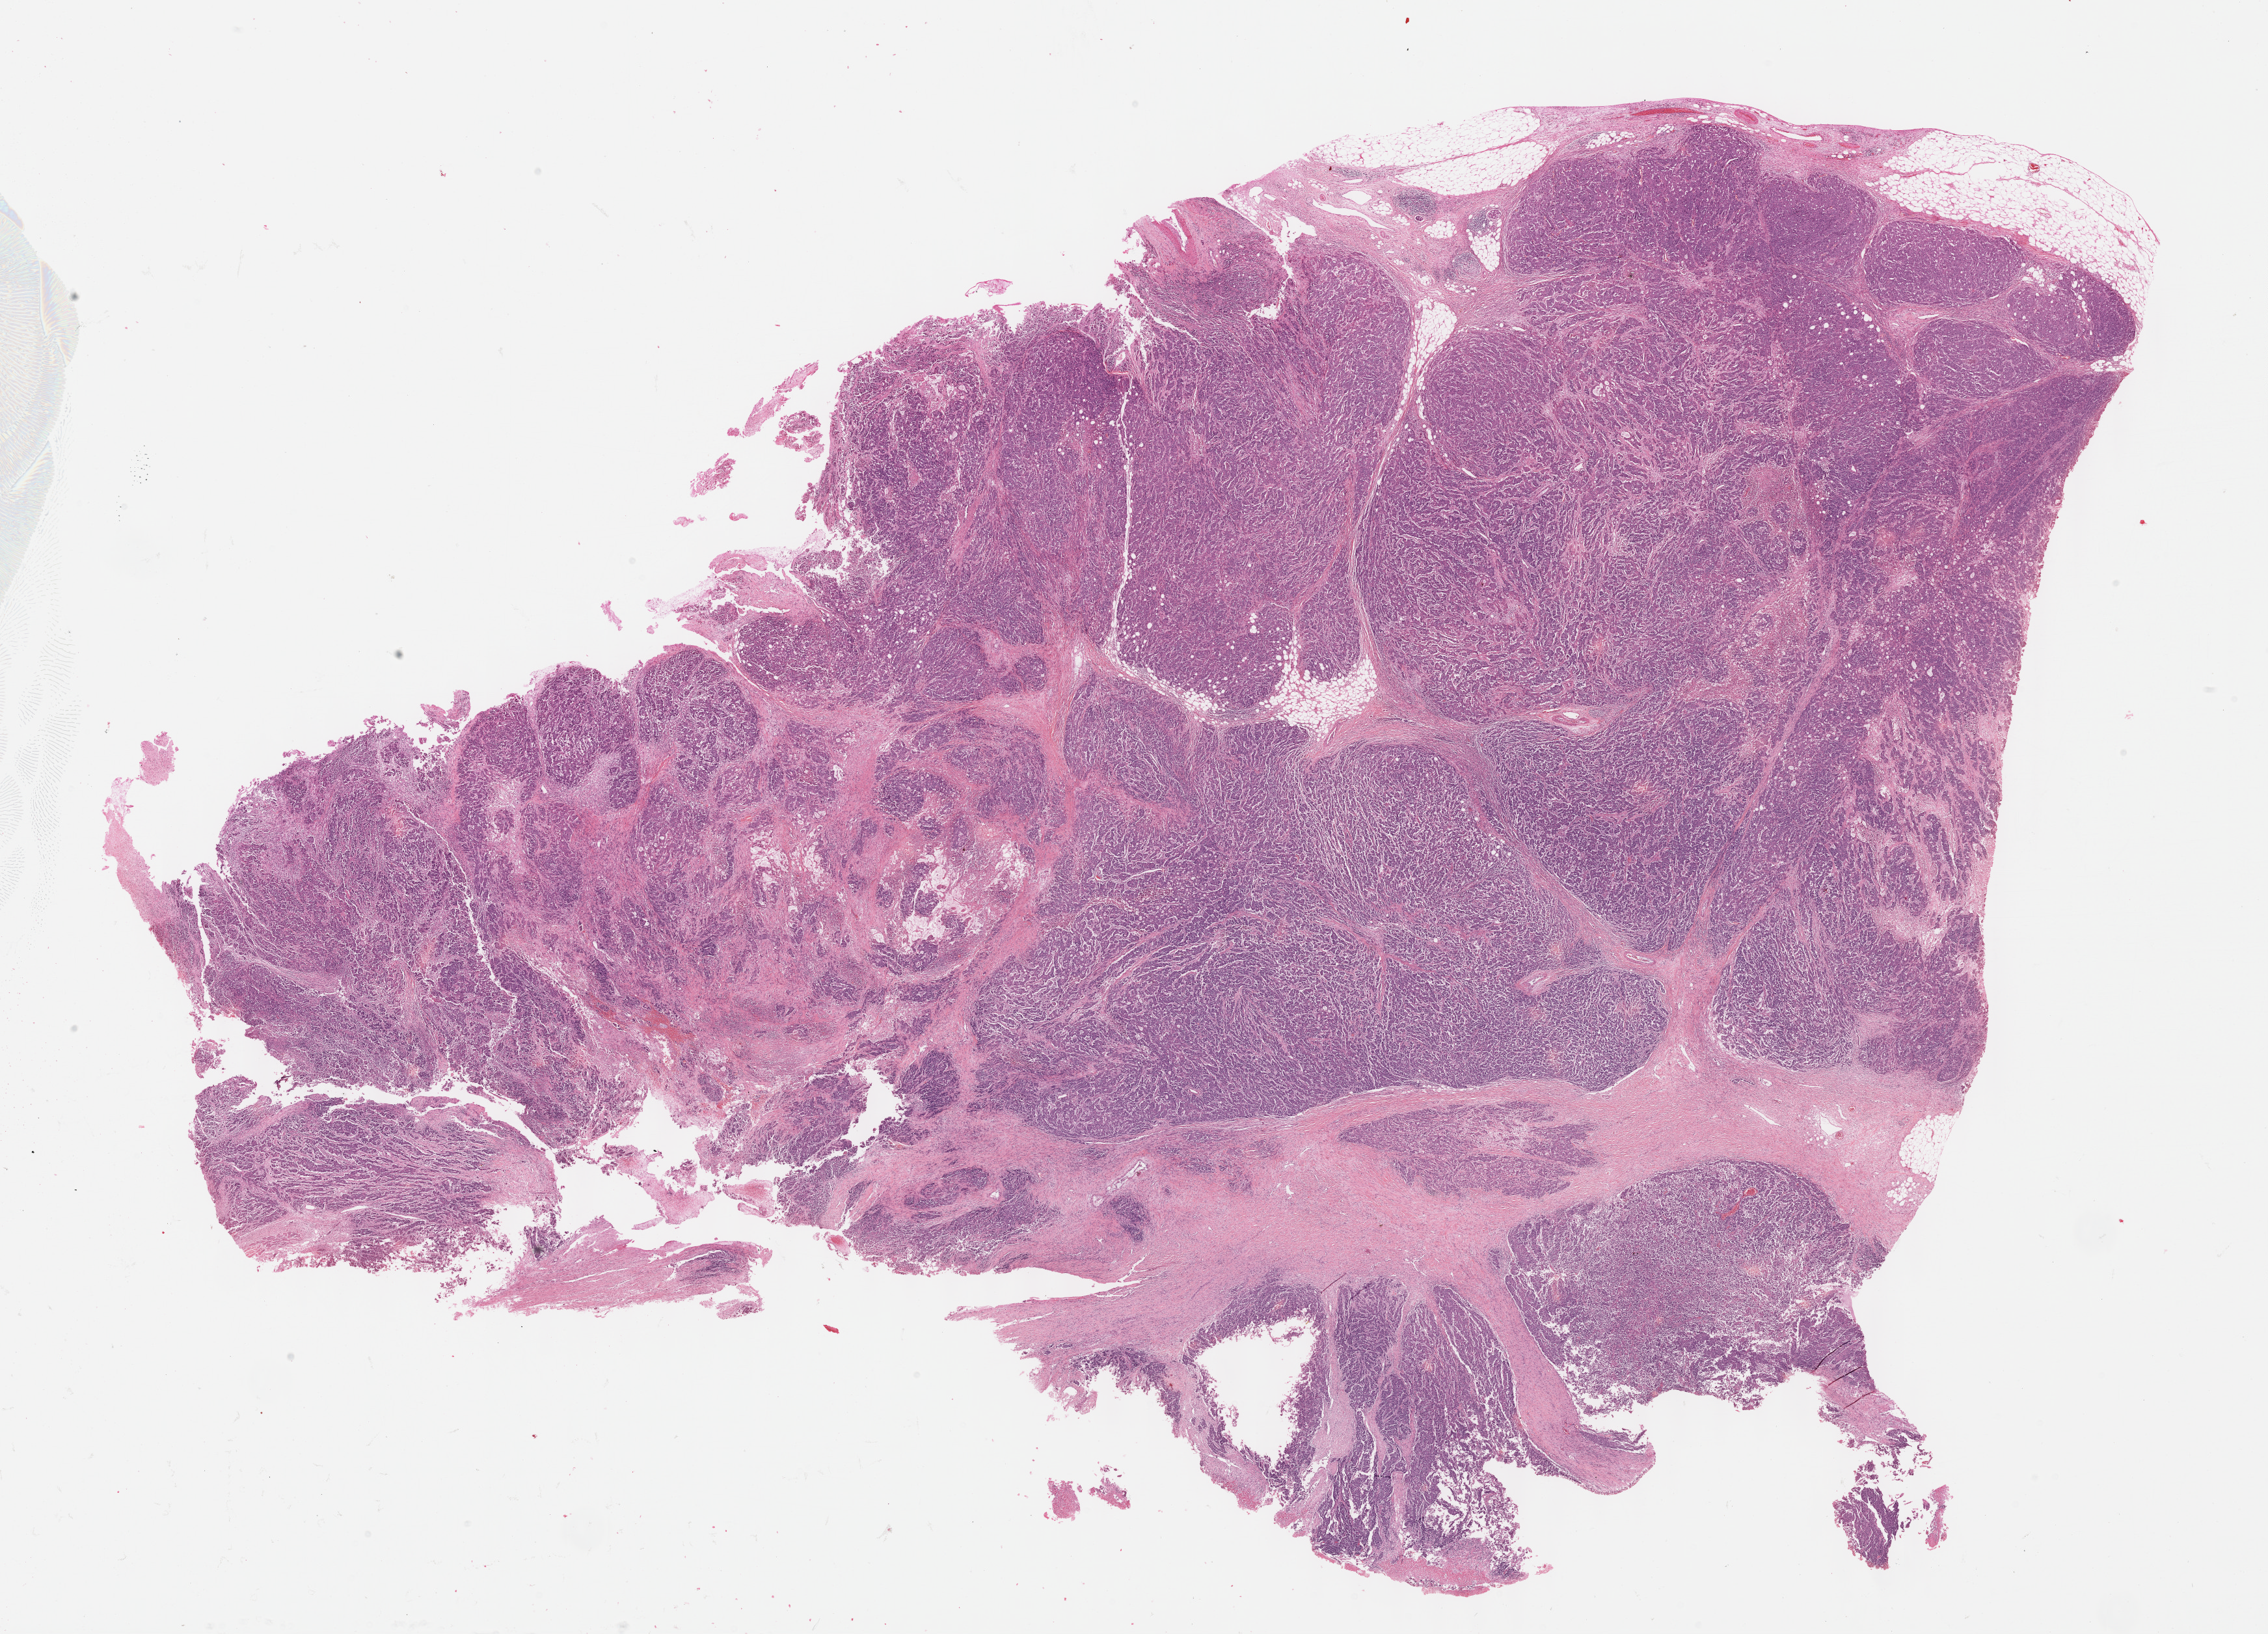
Whole-slide histology image, Hematoxylin and eosin (H&E) stained, shown as a low-resolution overview of the whole scanned area (about 28.2 x 20.3 mm). FFPE section. Sample: primary tumour, colon. Patient: female, age at initial diagnosis 40 years.
- lymph nodes positive (case pathology): 10 of 11 examined
- AJCC pathologic stage: IV (6th edition)
- pathologic diagnosis: Adenocarcinoma, NOS